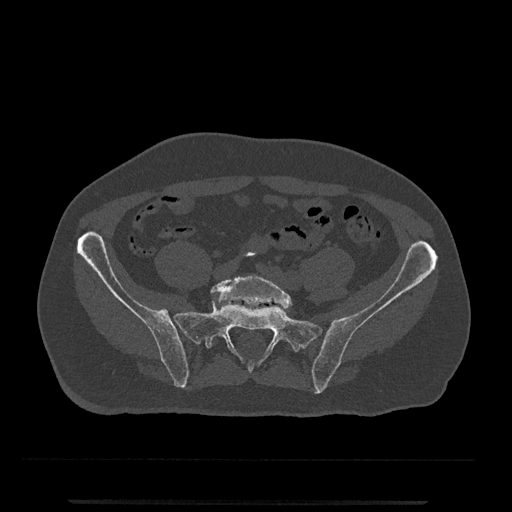
CT including the spine, one axial slice. Slice 31 of 797 in the series (ordered by position). Reconstruction kernel Br40s/3. 120 kVp. Bone window (W 1800 / L 400 HU). 0.5 mm slice thickness. 512 × 512 image matrix, field of view 419 × 419 mm. Patient: male, 63 years. From the clinical record (not read from this slice): primary cancer: prostate.
Annotated regions visible in this slice (semi-automatic segmentation, software-assisted and operator-edited):
- L5 vertebra: bounding box (x1, y1, x2, y2) in pixels: (211, 275, 293, 309)